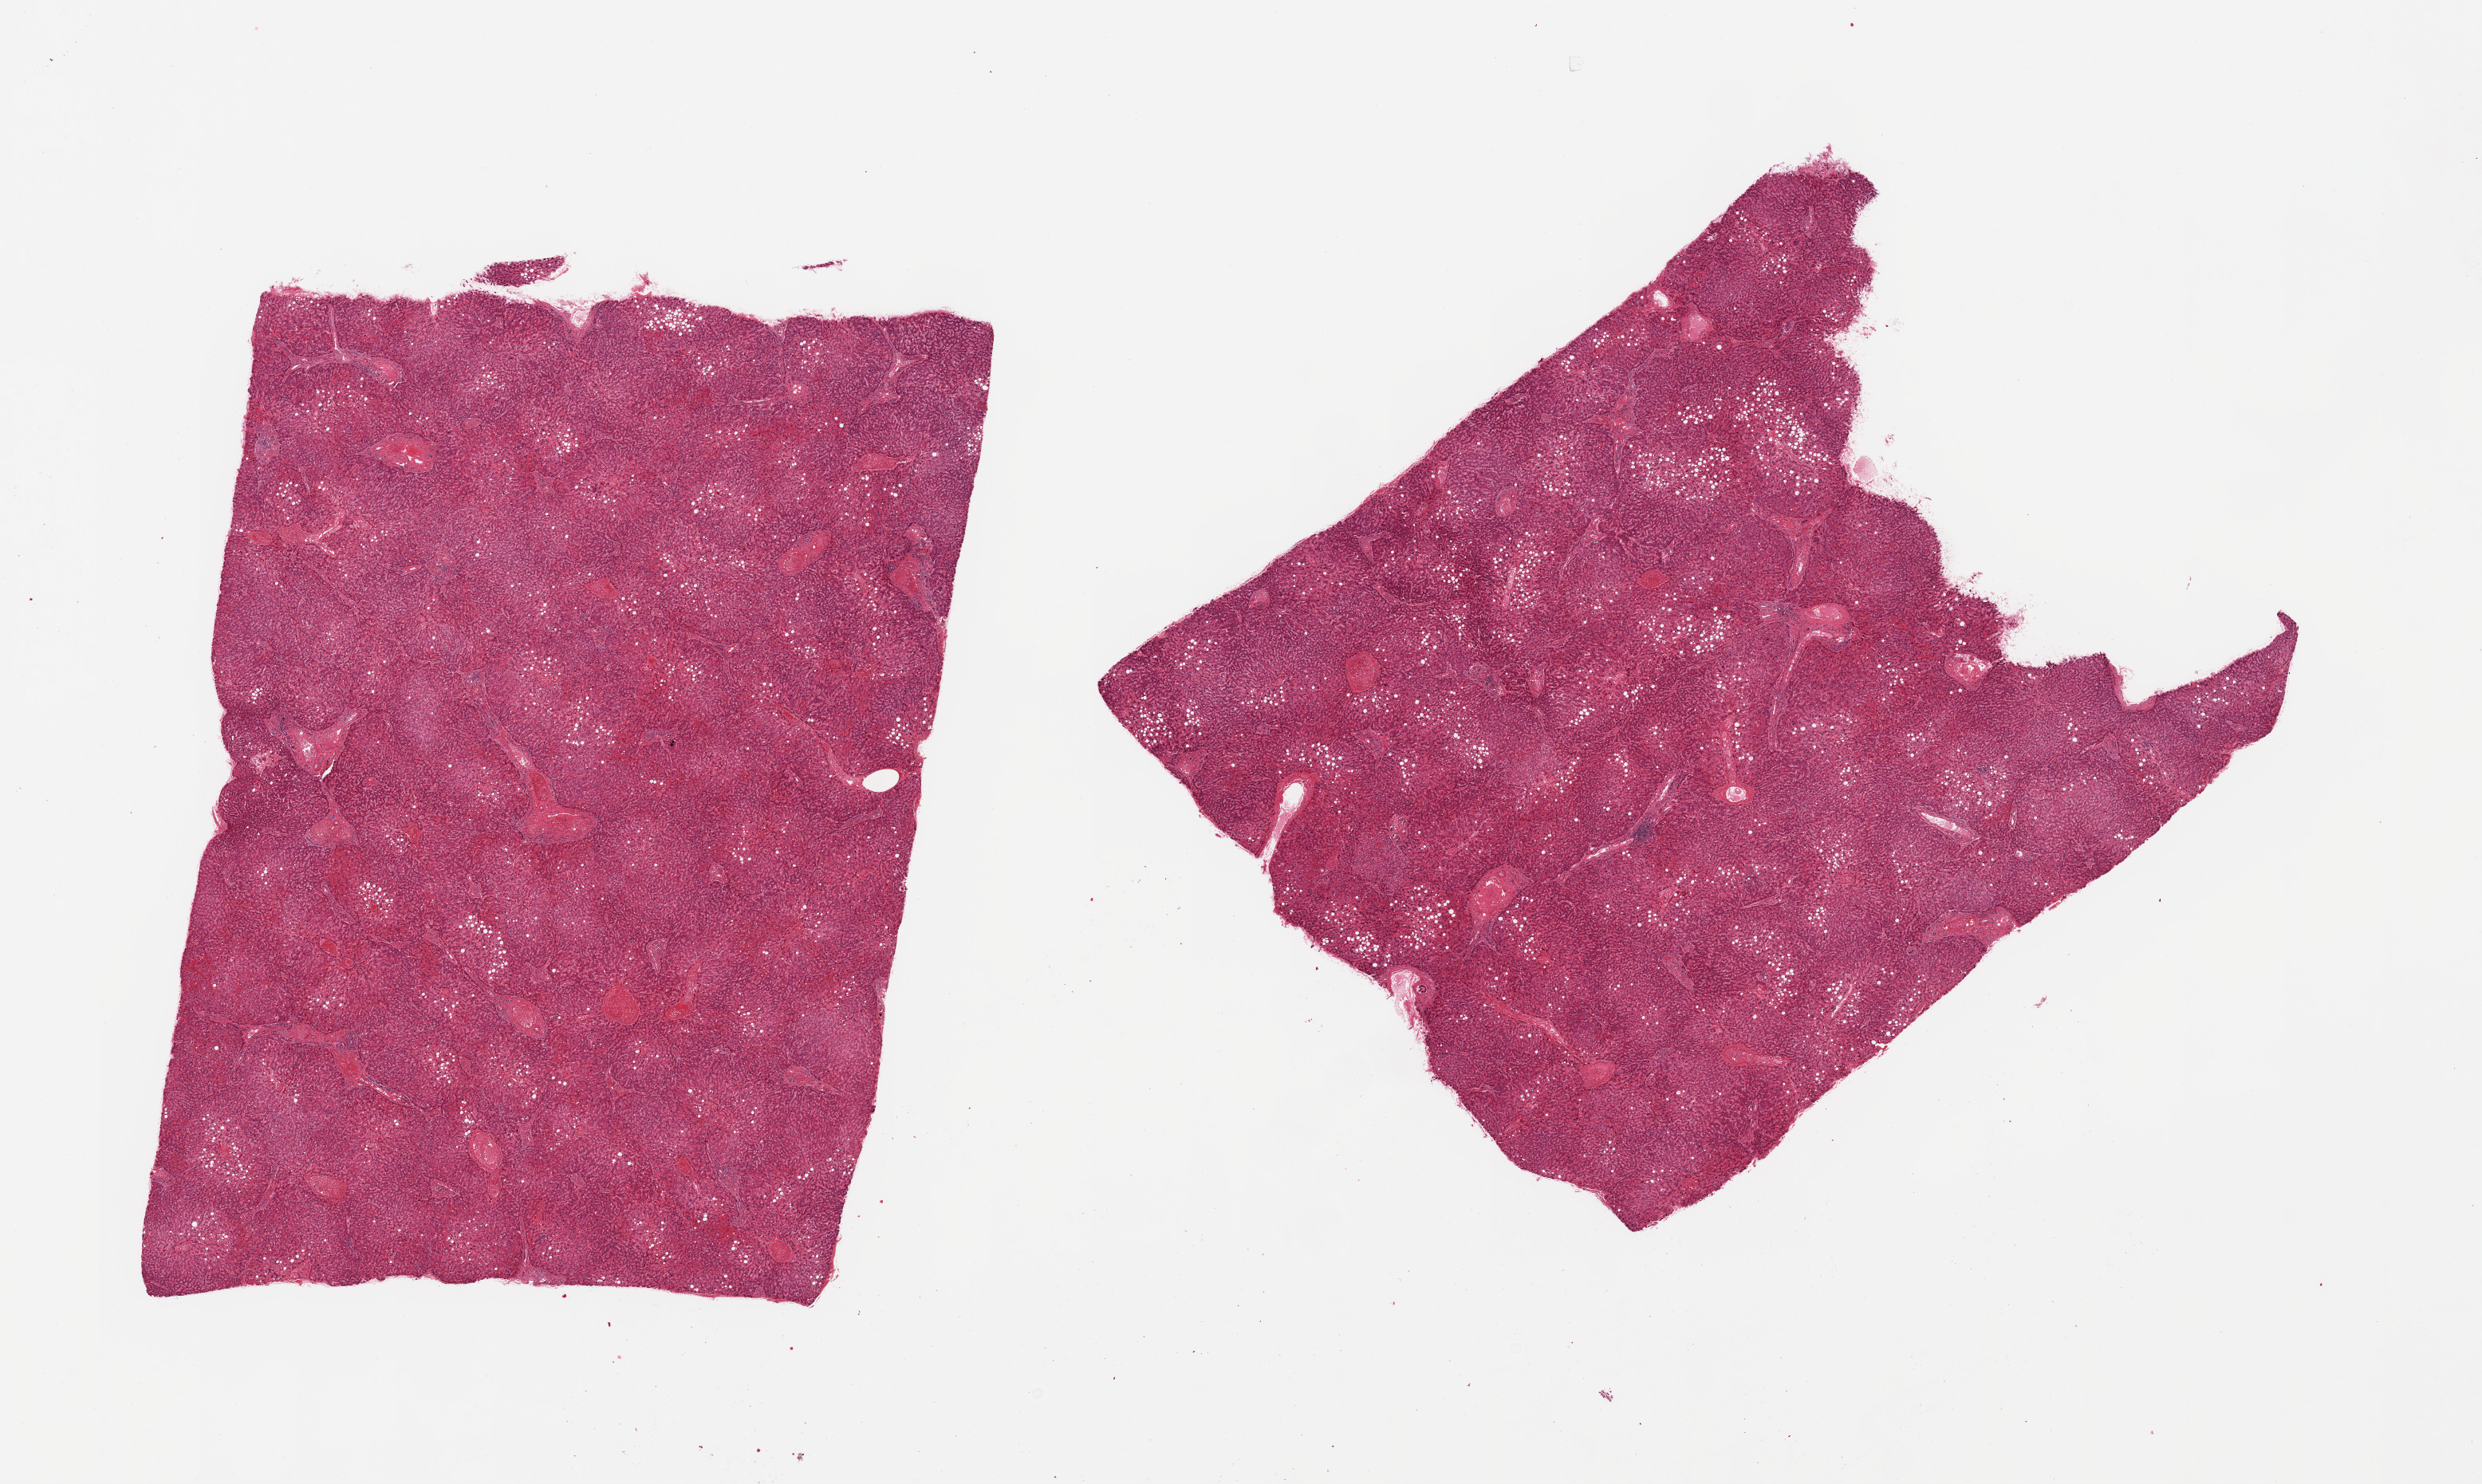
Whole-slide image, hematoxylin and eosin (H&E) stain, whole scanned area (about 24.6 x 14.7 mm, acquisition: 20x scan) shown as a low-resolution overview, PAXgene-fixed, paraffin-embedded tissue, section of liver (target tissue), tissue donor sample.
Pathologist's review note for this sample: 2 pieces; some congestion and steatosis.